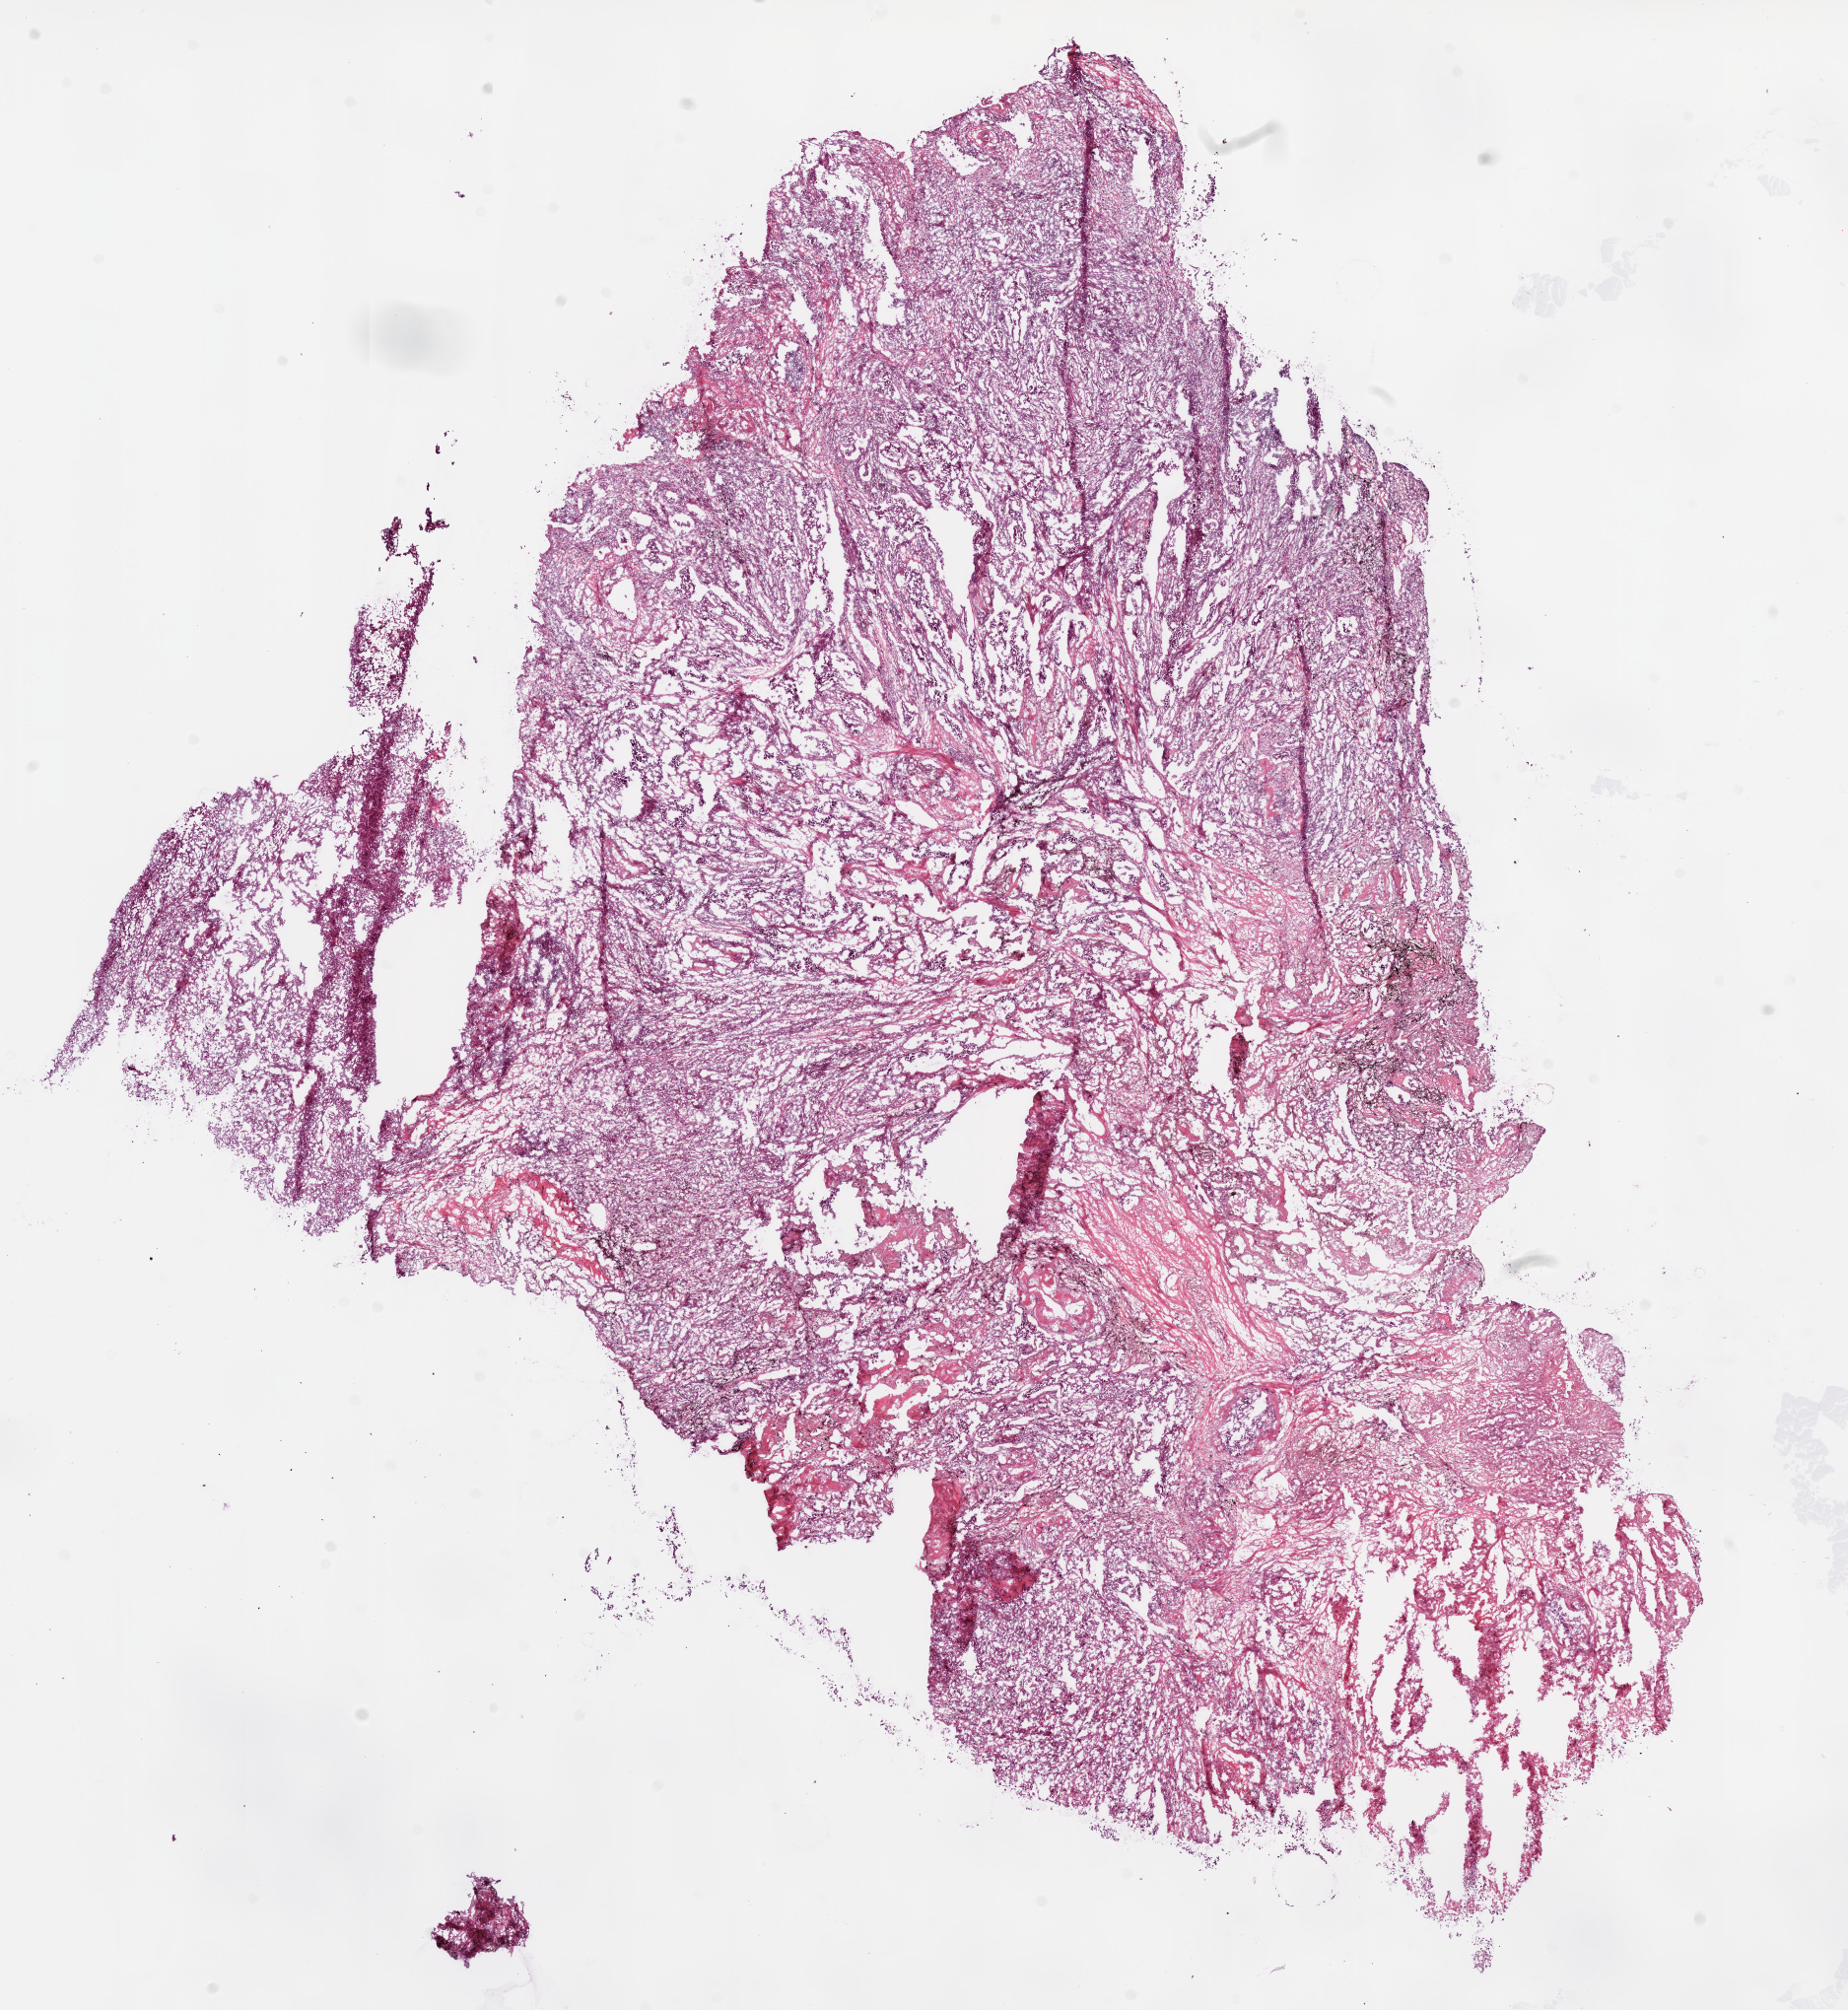
Digitized Hematoxylin and eosin (H&E) stained tissue section (whole slide), a low-resolution overview of the entire scanned area, about 15.0 x 16.4 mm (acquisition: 20x scan), frozen section from the top of the tissue portion, sample: primary tumour, lung. Patient: male, age at initial diagnosis 72 years. Pathologist review of this section (percent, as recorded): tumour cells 80%, tumour nuclei 70%, normal cells 0%, stromal cells 15%, necrosis 5%.
- diagnosis: Adenocarcinoma with mixed subtypes (upper lobe, lung)
- AJCC pathologic stage: IB
- laterality: right